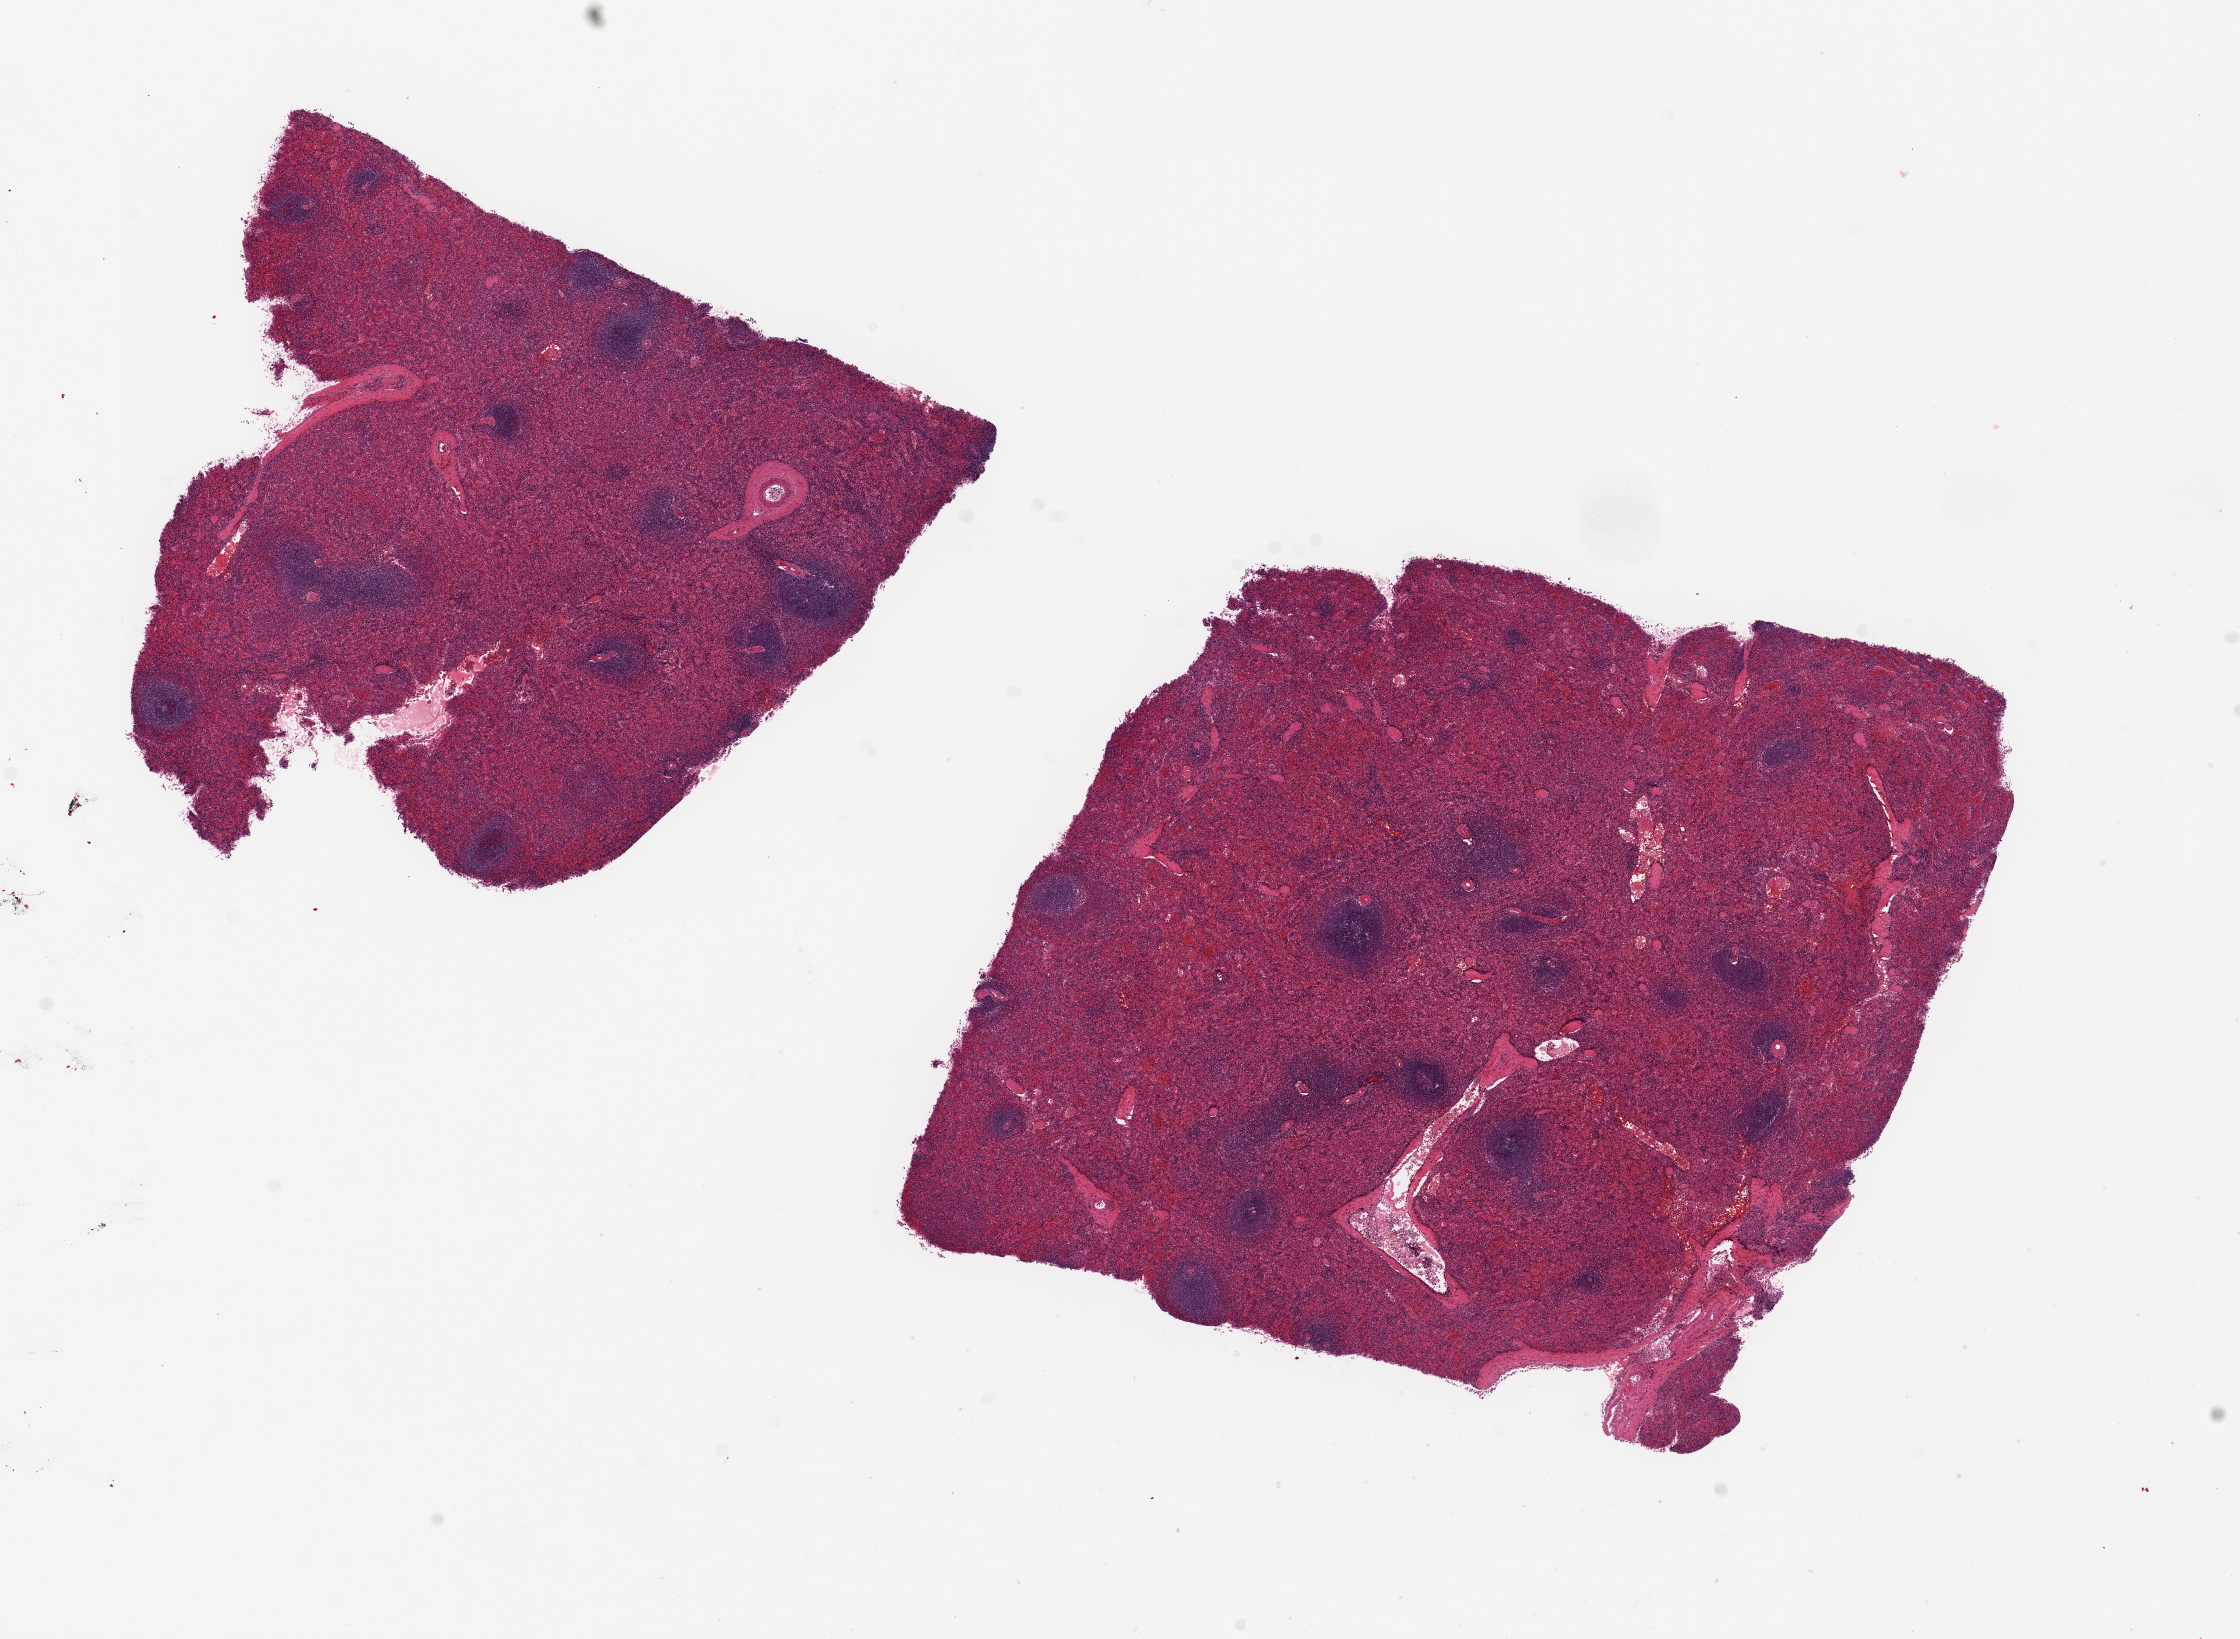
Hematoxylin and eosin (H&E) whole-slide image — a low-resolution overview of the entire scanned area, about 17.7 x 13.0 mm. PAXgene-fixed, paraffin-embedded tissue. Sampled site (target tissue): spleen. Donor tissue sample. Donor sex: female.
Pathologist's review note for this sample: 2 pieces, ~6 mm cubed; moderate congestion.